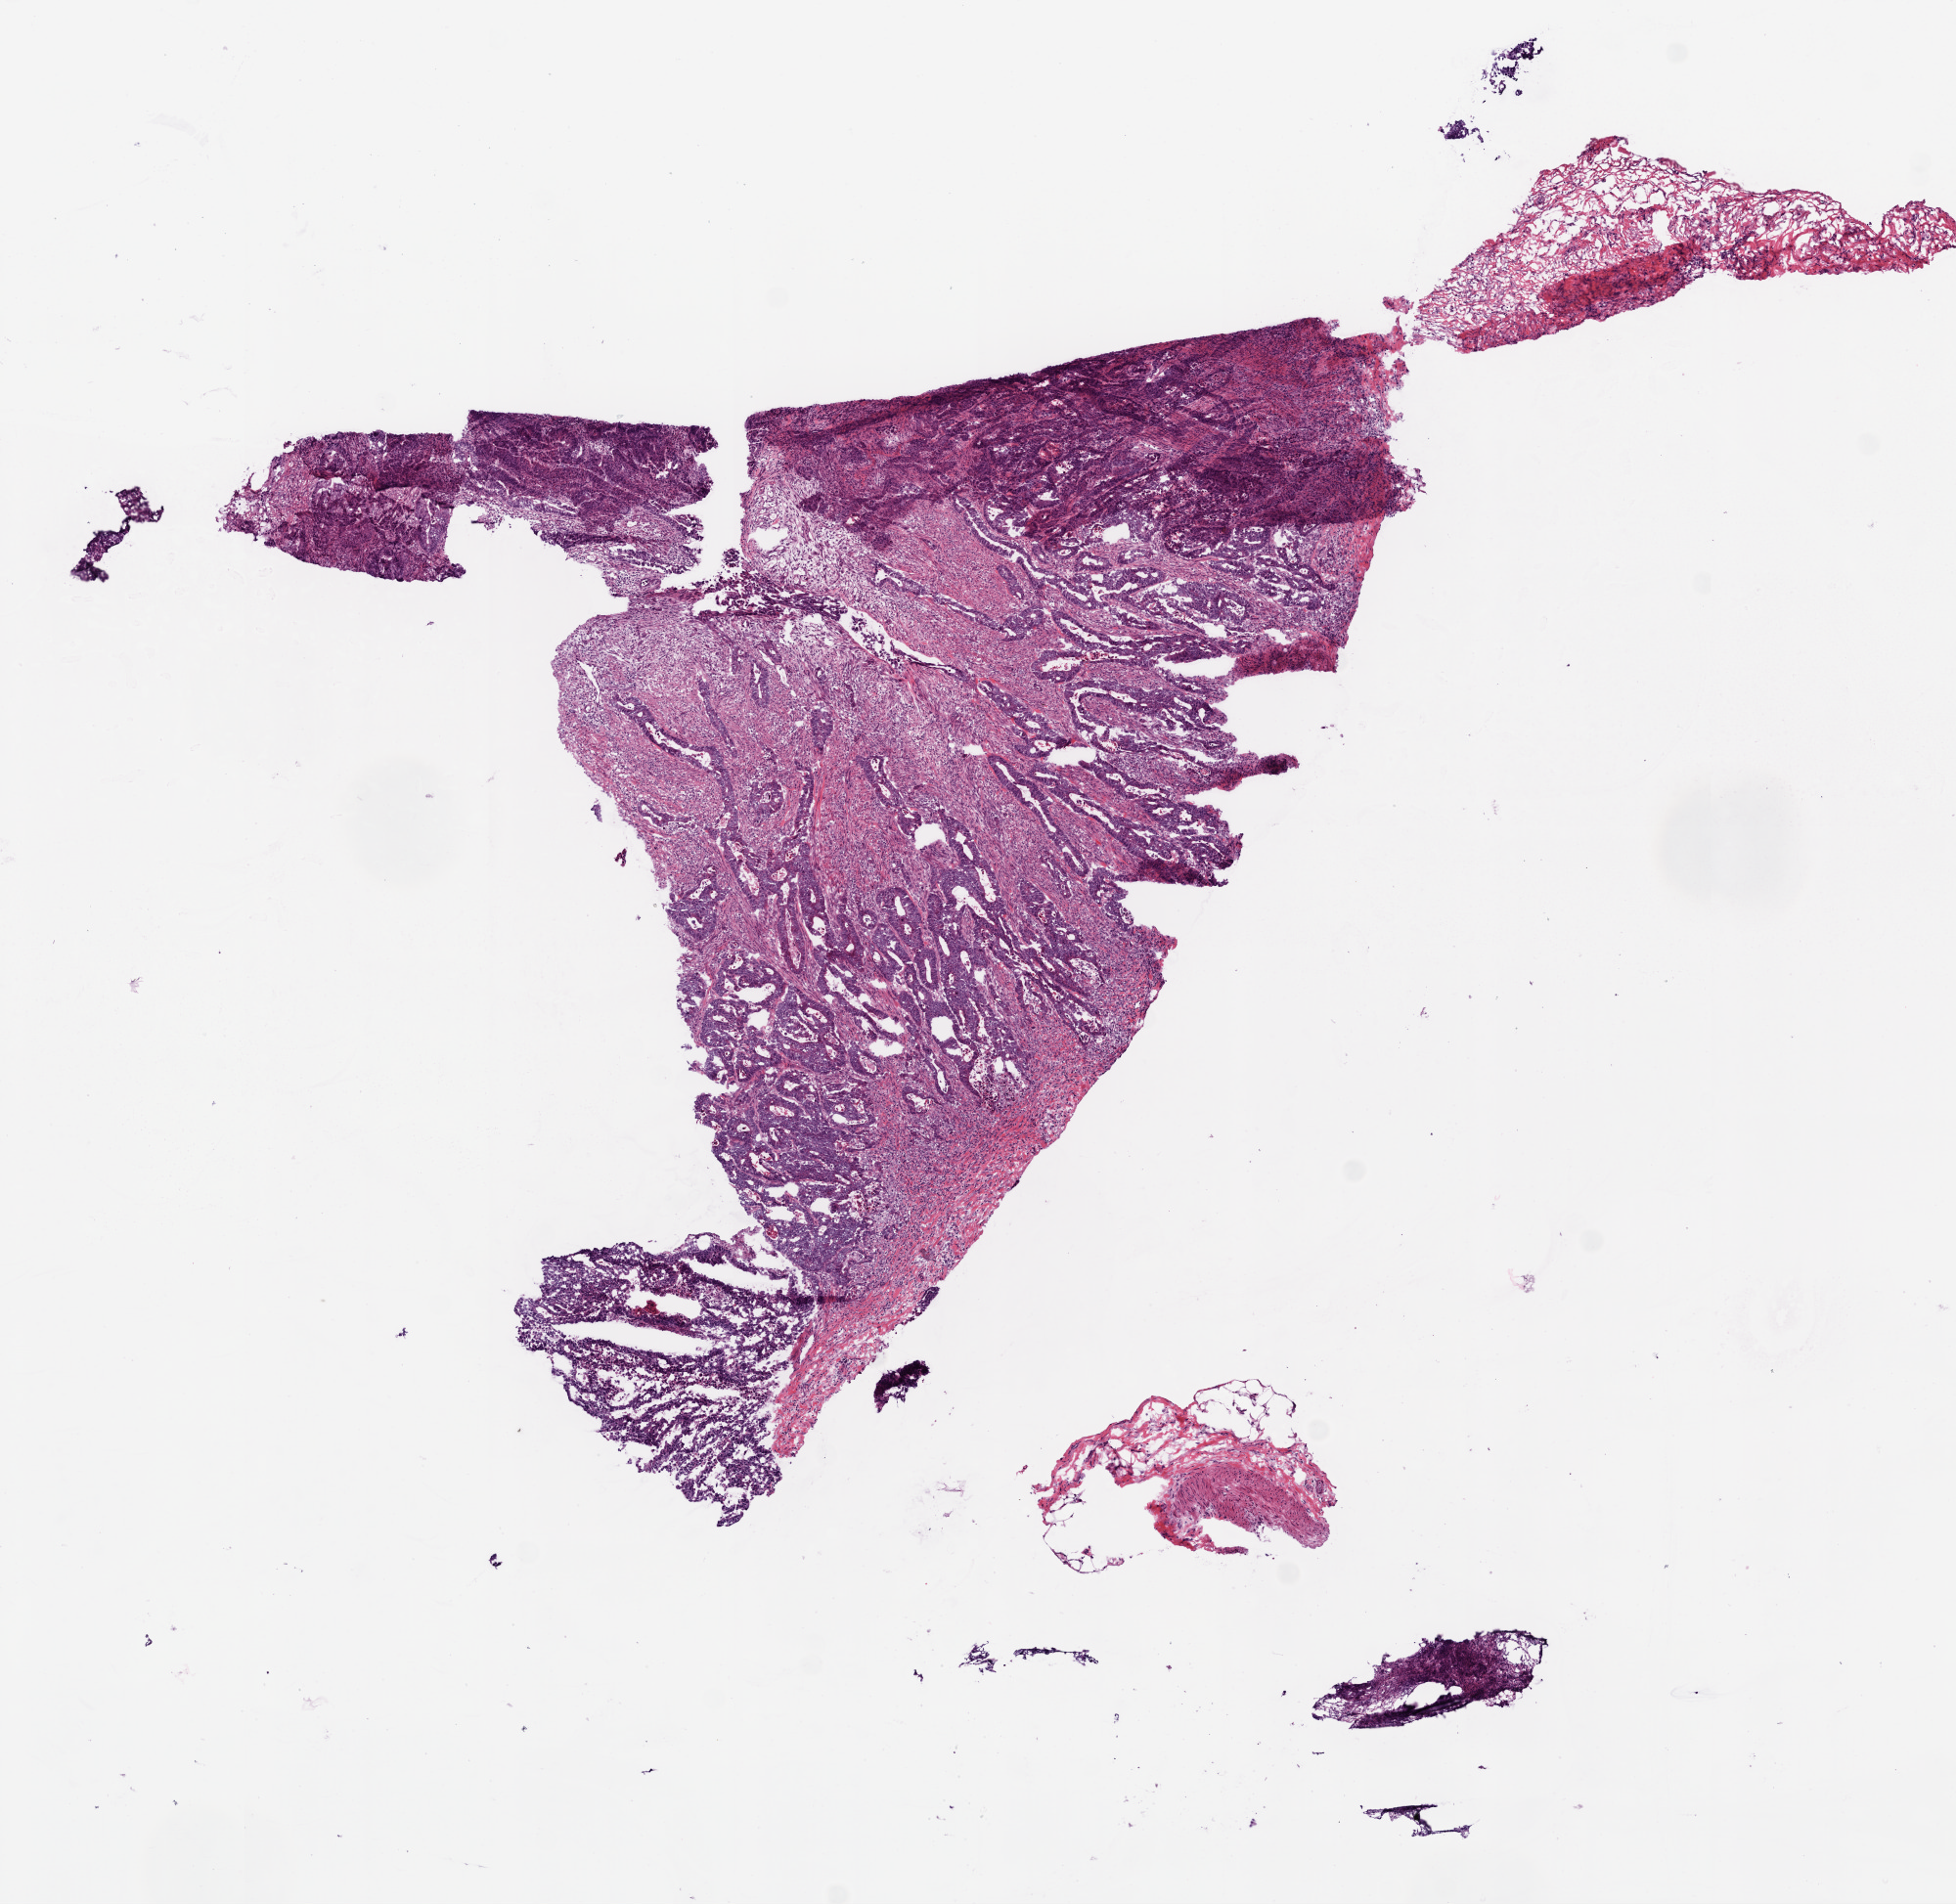
Whole-slide histology image, Hematoxylin and eosin (H&E) stained, a low-resolution overview of the entire scanned area, about 8.0 x 7.8 mm (from a 20x scan), frozen section, sample: primary tumour, rectum. Female patient; age at initial diagnosis 74 years. Slide review estimates, as recorded: tumour cells 65%, tumour nuclei 75%, normal cells 0%, stromal cells 30%, necrosis 5%.
* pathologic diagnosis: Adenocarcinoma, NOS
* AJCC pathologic stage: IIA (6th edition)